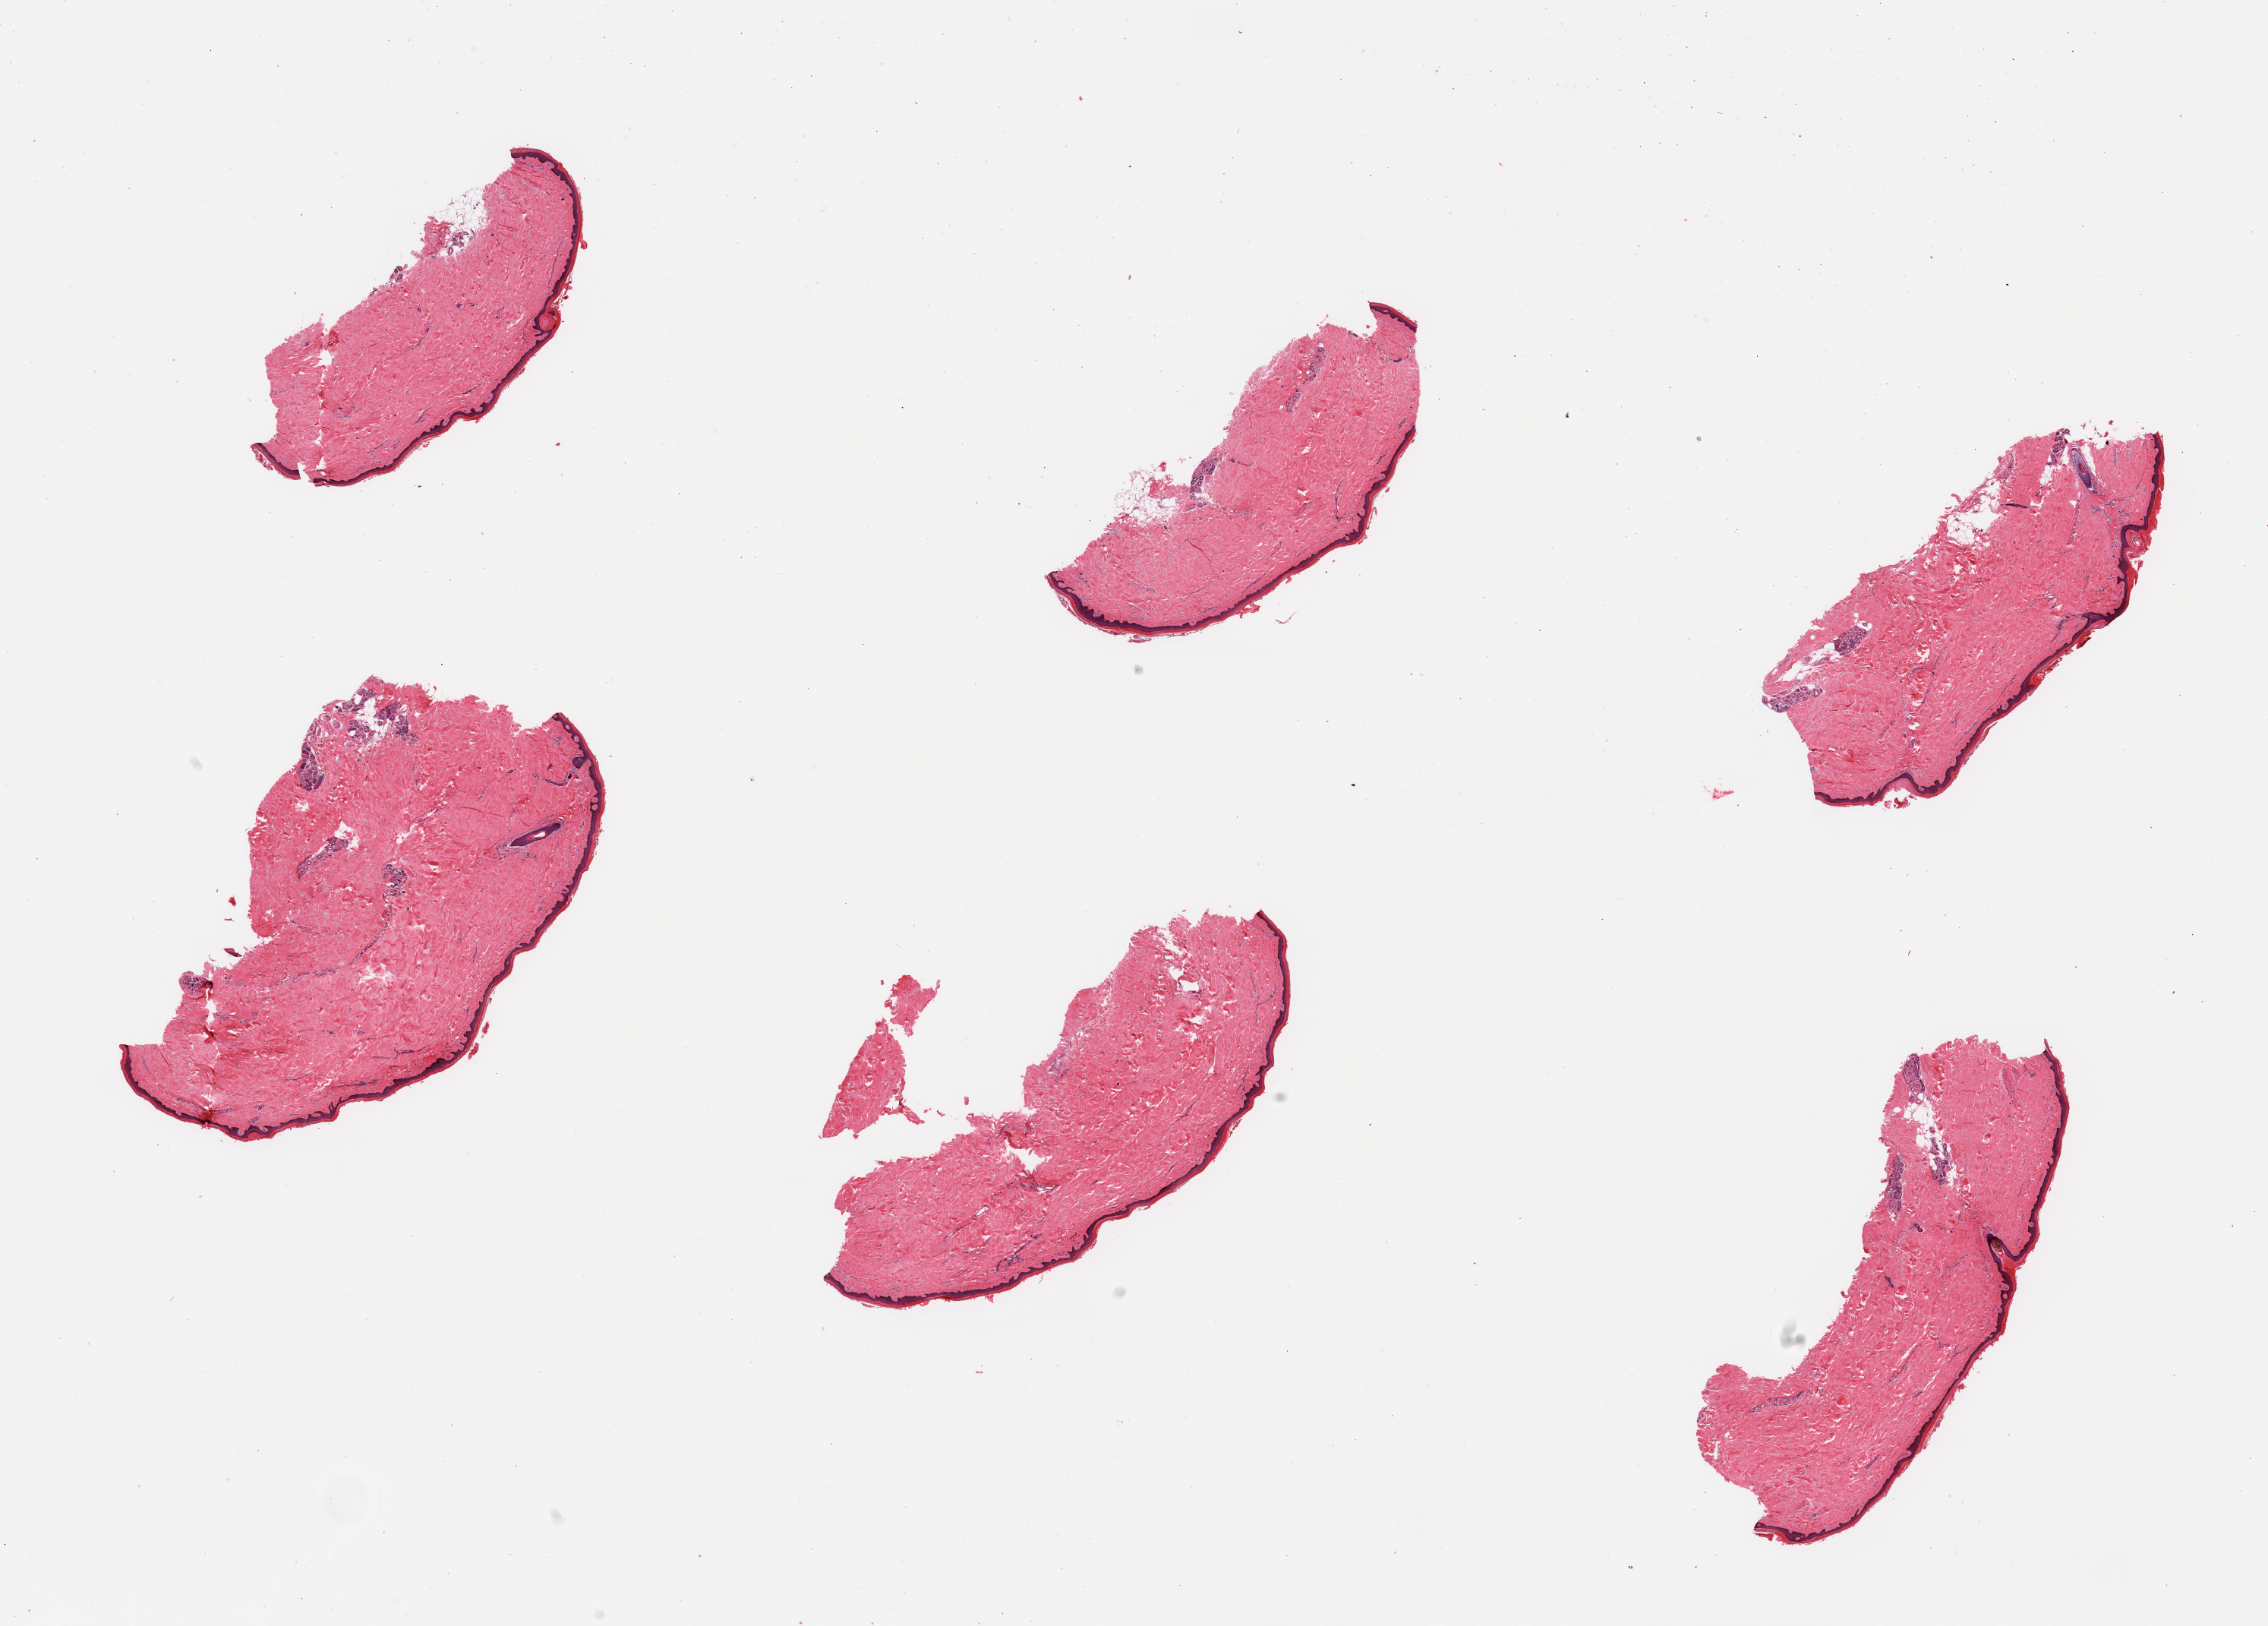
Digitized H&E-stained section — low-resolution overview of the scanned area, about 23.6 x 16.9 mm, PAXgene-fixed, paraffin-embedded tissue, target tissue: skin of lower leg, donor tissue sample. Male donor.
• reviewer comment on this tissue sample: 6 pieces, no dermal fat; squamous epithelium is ~50 microns